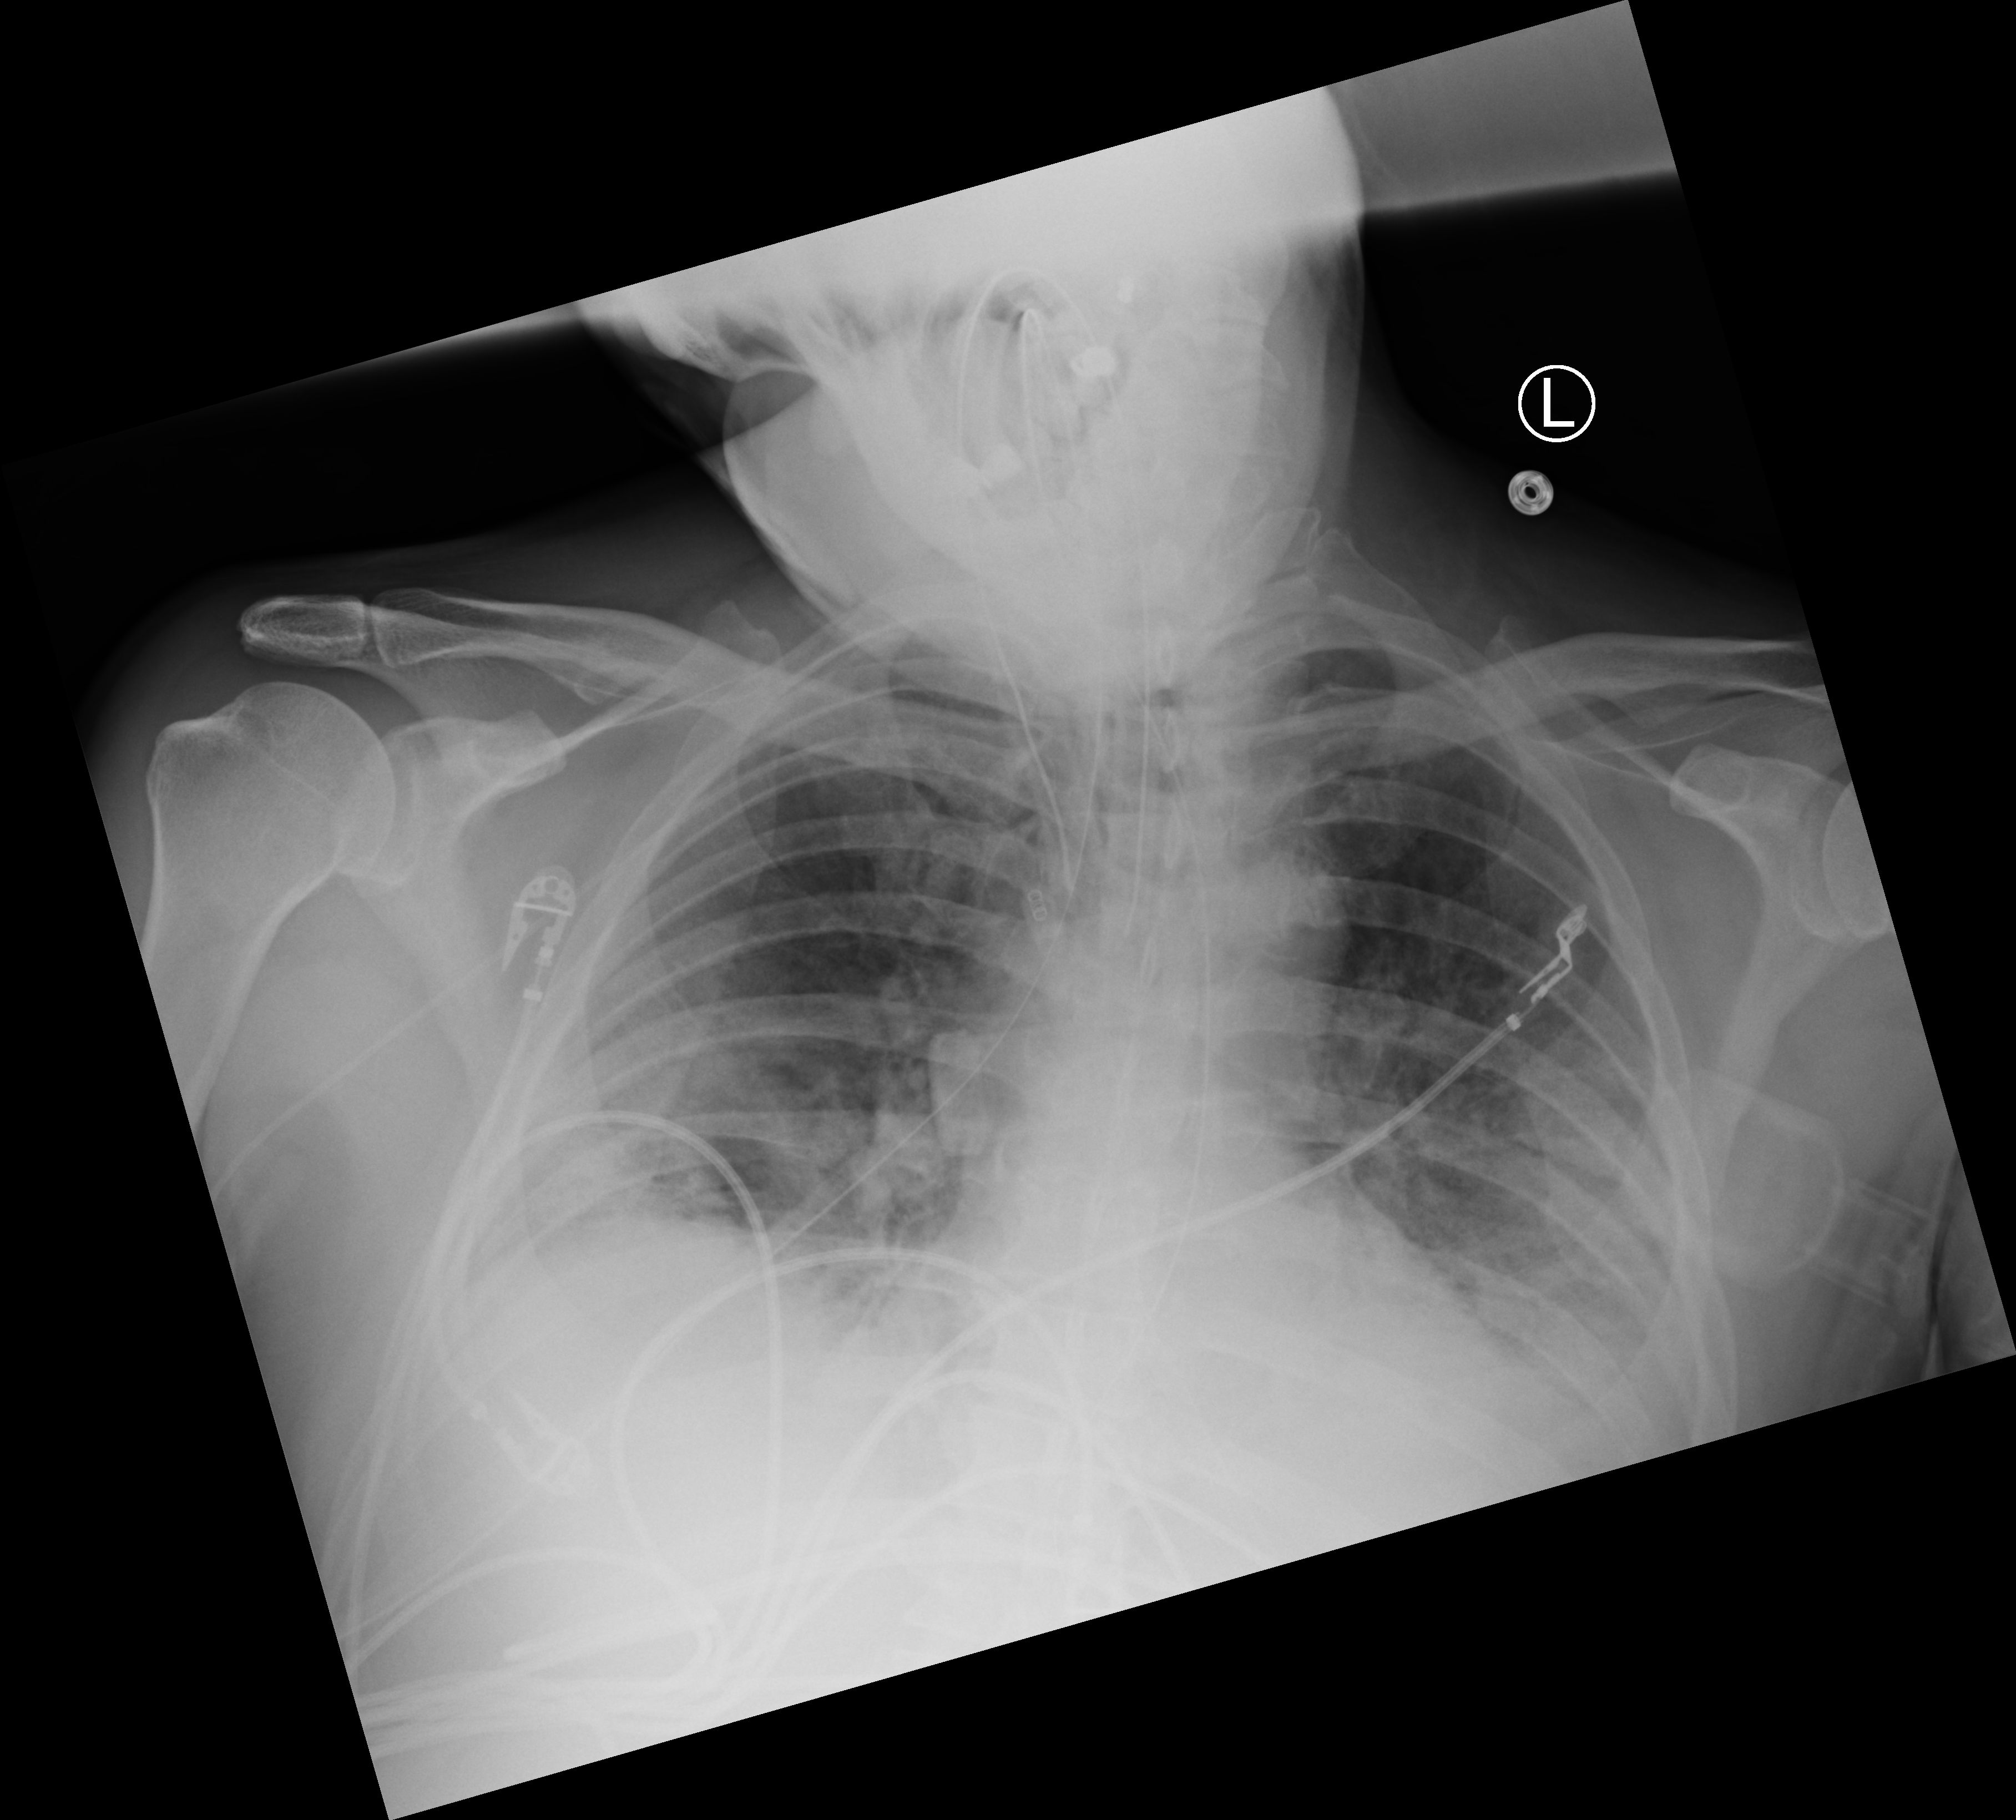
Chest X-ray (portable); anteroposterior (AP) projection. Male patient hospitalised with COVID-19, age 60–74 years.
From the hospital-stay record, not from the radiograph (when in the stay this image was taken is not recorded): length of hospital stay: 26 days.